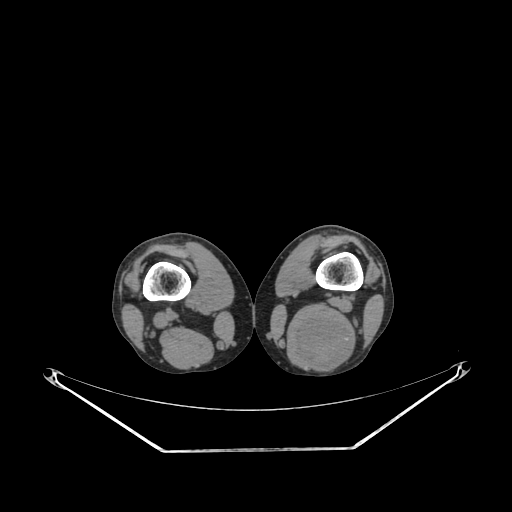
CT of an extremity soft-tissue mass (from a PET/CT study), one axial slice. Position 194 of 267 along the scan axis. 140 kVp. Soft-tissue window (W 400 / L 40 HU). 3.75 mm slice thickness. 512 × 512 image matrix, field of view 500 × 500 mm. Male patient. Case-level facts recorded for this patient, not image findings: histological type: synovial sarcoma; site of the primary tumour: left poplietal fossa.
Structures marked on this image (expert contour drawn on MRI and transferred to this co-registered scan by the dataset authors):
- gross tumour volume (mass): box from (x=292, y=317) to (x=355, y=369) px